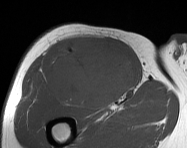
MRI of an extremity soft-tissue mass, one axial slice. Position 96 of 114 along the scan axis. MR volume resampled by the dataset authors to the PET/CT grid (not the native acquisition matrix). 187 × 148 image matrix, field of view 183 × 145 mm. Male patient. Case-level facts recorded for this patient, not image findings: histological type: pleiomorphic leiomyosarcoma; grade: intermediate; site of the primary tumour: right thigh.
Outlined on this slice (expert contour drawn on MRI and transferred to this co-registered scan by the dataset authors):
- gross tumour volume including surrounding oedema: box from (x=48, y=36) to (x=135, y=108) px
- gross tumour volume (mass): (x=50, y=36)–(x=135, y=108)